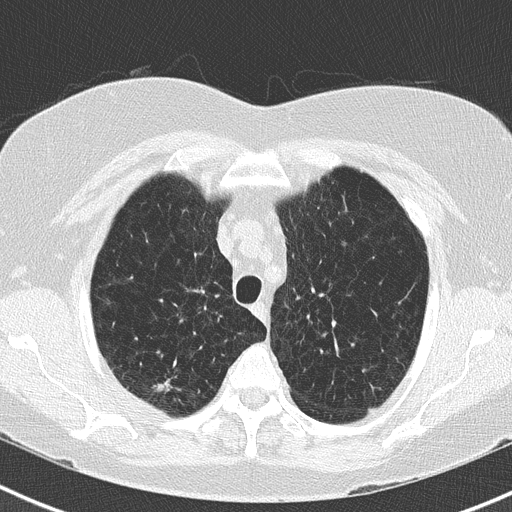
Axial slice from a low-dose chest CT screening exam. Second screening round (one year after baseline). Lung window (W 1500 / L -600 HU). Lung (sharp) reconstruction kernel (B50f). Slice 43 of 183 in the series. 512 × 512 image matrix. Female, age 73 years at enrolment. Former smoker at enrolment.
Expert-annotated lung lesion, bounding box (x1, y1, x2, y2) in pixels: (134, 356, 191, 405). The screening reader recorded 2 non-calcified nodules or masses ≥4 mm on this exam (right upper lobe, right upper lobe); which of them this box marks is not recorded. Official screen result: positive, no significant change: stable abnormalities potentially related to lung cancer, unchanged since the prior screening exam. Lung cancer was diagnosed 250 days after this screen: adenocarcinoma, NOS, right upper lobe, moderately differentiated (G2), stage IB (AJCC 6th edition), 15 mm at pathology.